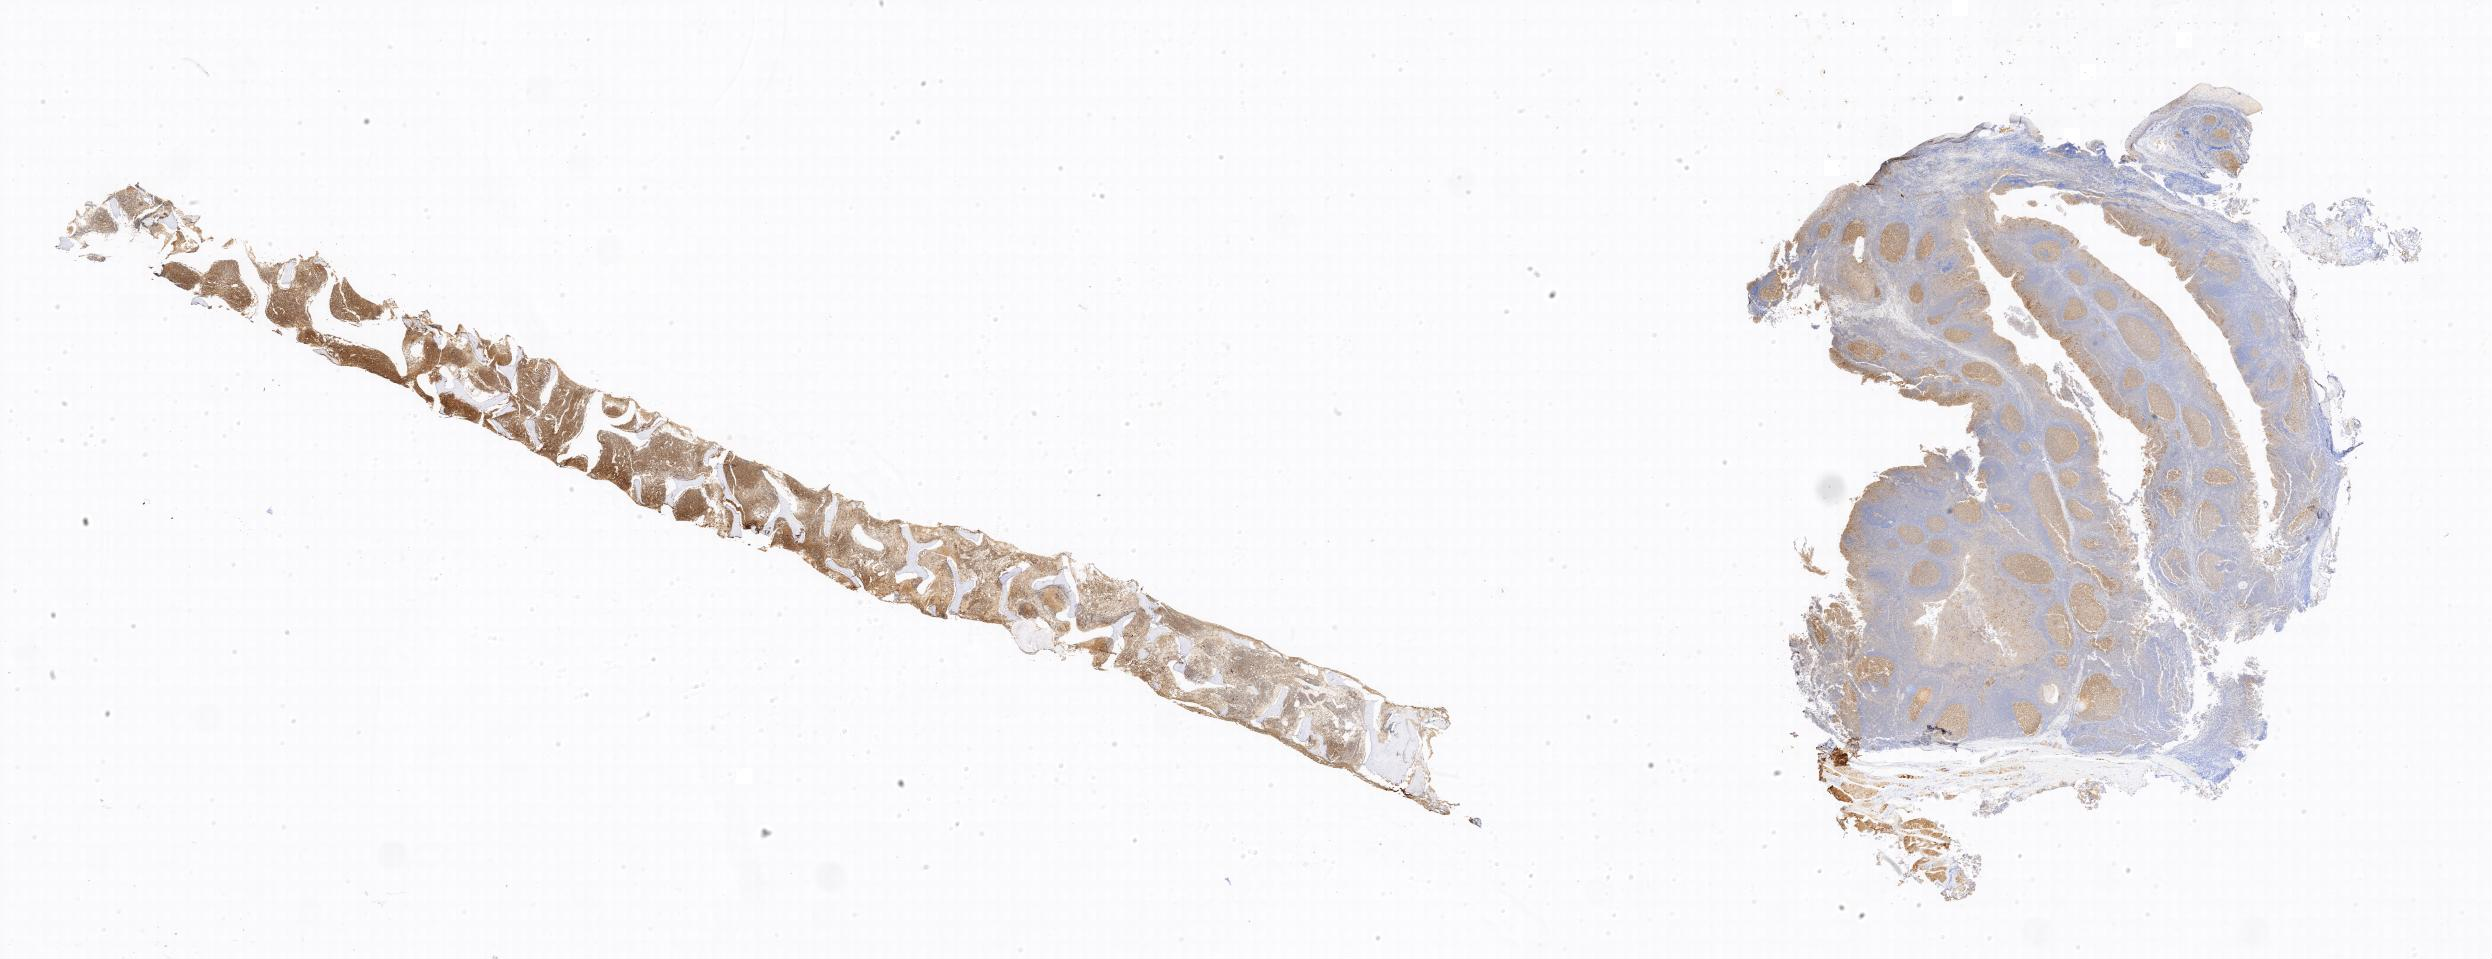
Whole-slide image, immunohistochemical stain for BCL6, a low-resolution overview of the entire scanned area. Specimen: tumor tissue. Site: bone marrow. Male patient, age 18 years.
* histologic diagnosis: Burkitt lymphoma, NOS